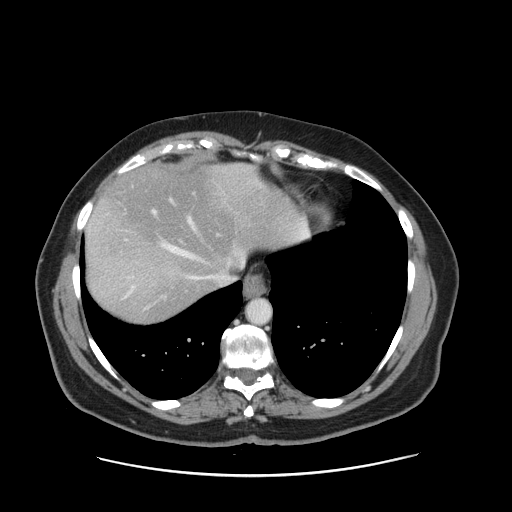
Contrast-enhanced abdominal CT, one axial slice; position 130 of 161 along the scan axis; 120 kVp; intravenous contrast given; soft-tissue window (W 400 / L 40 HU); 2.5 mm slice thickness; 512 × 512 image matrix. Female patient, age 62 years. Case-level facts recorded for this patient, not image findings: diagnosis: colorectal cancer liver metastases, imaged before liver resection.
Annotated regions visible in this slice (manually delineated by an expert):
- hepatic veins: bounding box [x1, y1, x2, y2] px = [127, 168, 251, 290]
- liver: [85, 163, 305, 323]
- planned liver remnant (the part of the liver to remain after resection): [94, 164, 305, 279]
- portal vein (with intrahepatic branches): [152, 197, 182, 243]